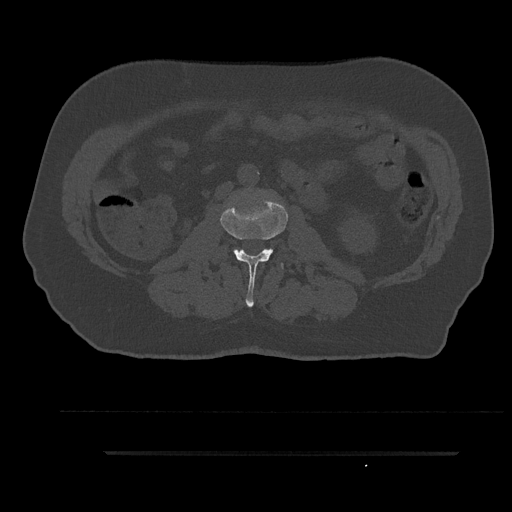
CT including the spine, one axial slice. Slice 94 of 797 in the series (ordered by position). 120 kVp. Bone window (W 1800 / L 400 HU). 0.5 mm slice thickness. 512 × 512 image matrix. Male patient, age 63 years. From the clinical record (not read from this slice): primary cancer: renal; vertebrae with lytic lesions (as recorded): T8.
Structures marked on this image (semi-automatic segmentation, software-assisted and operator-edited):
- L2 vertebra: bounding box <221,199,288,308> (left, top, right, bottom; pixels)